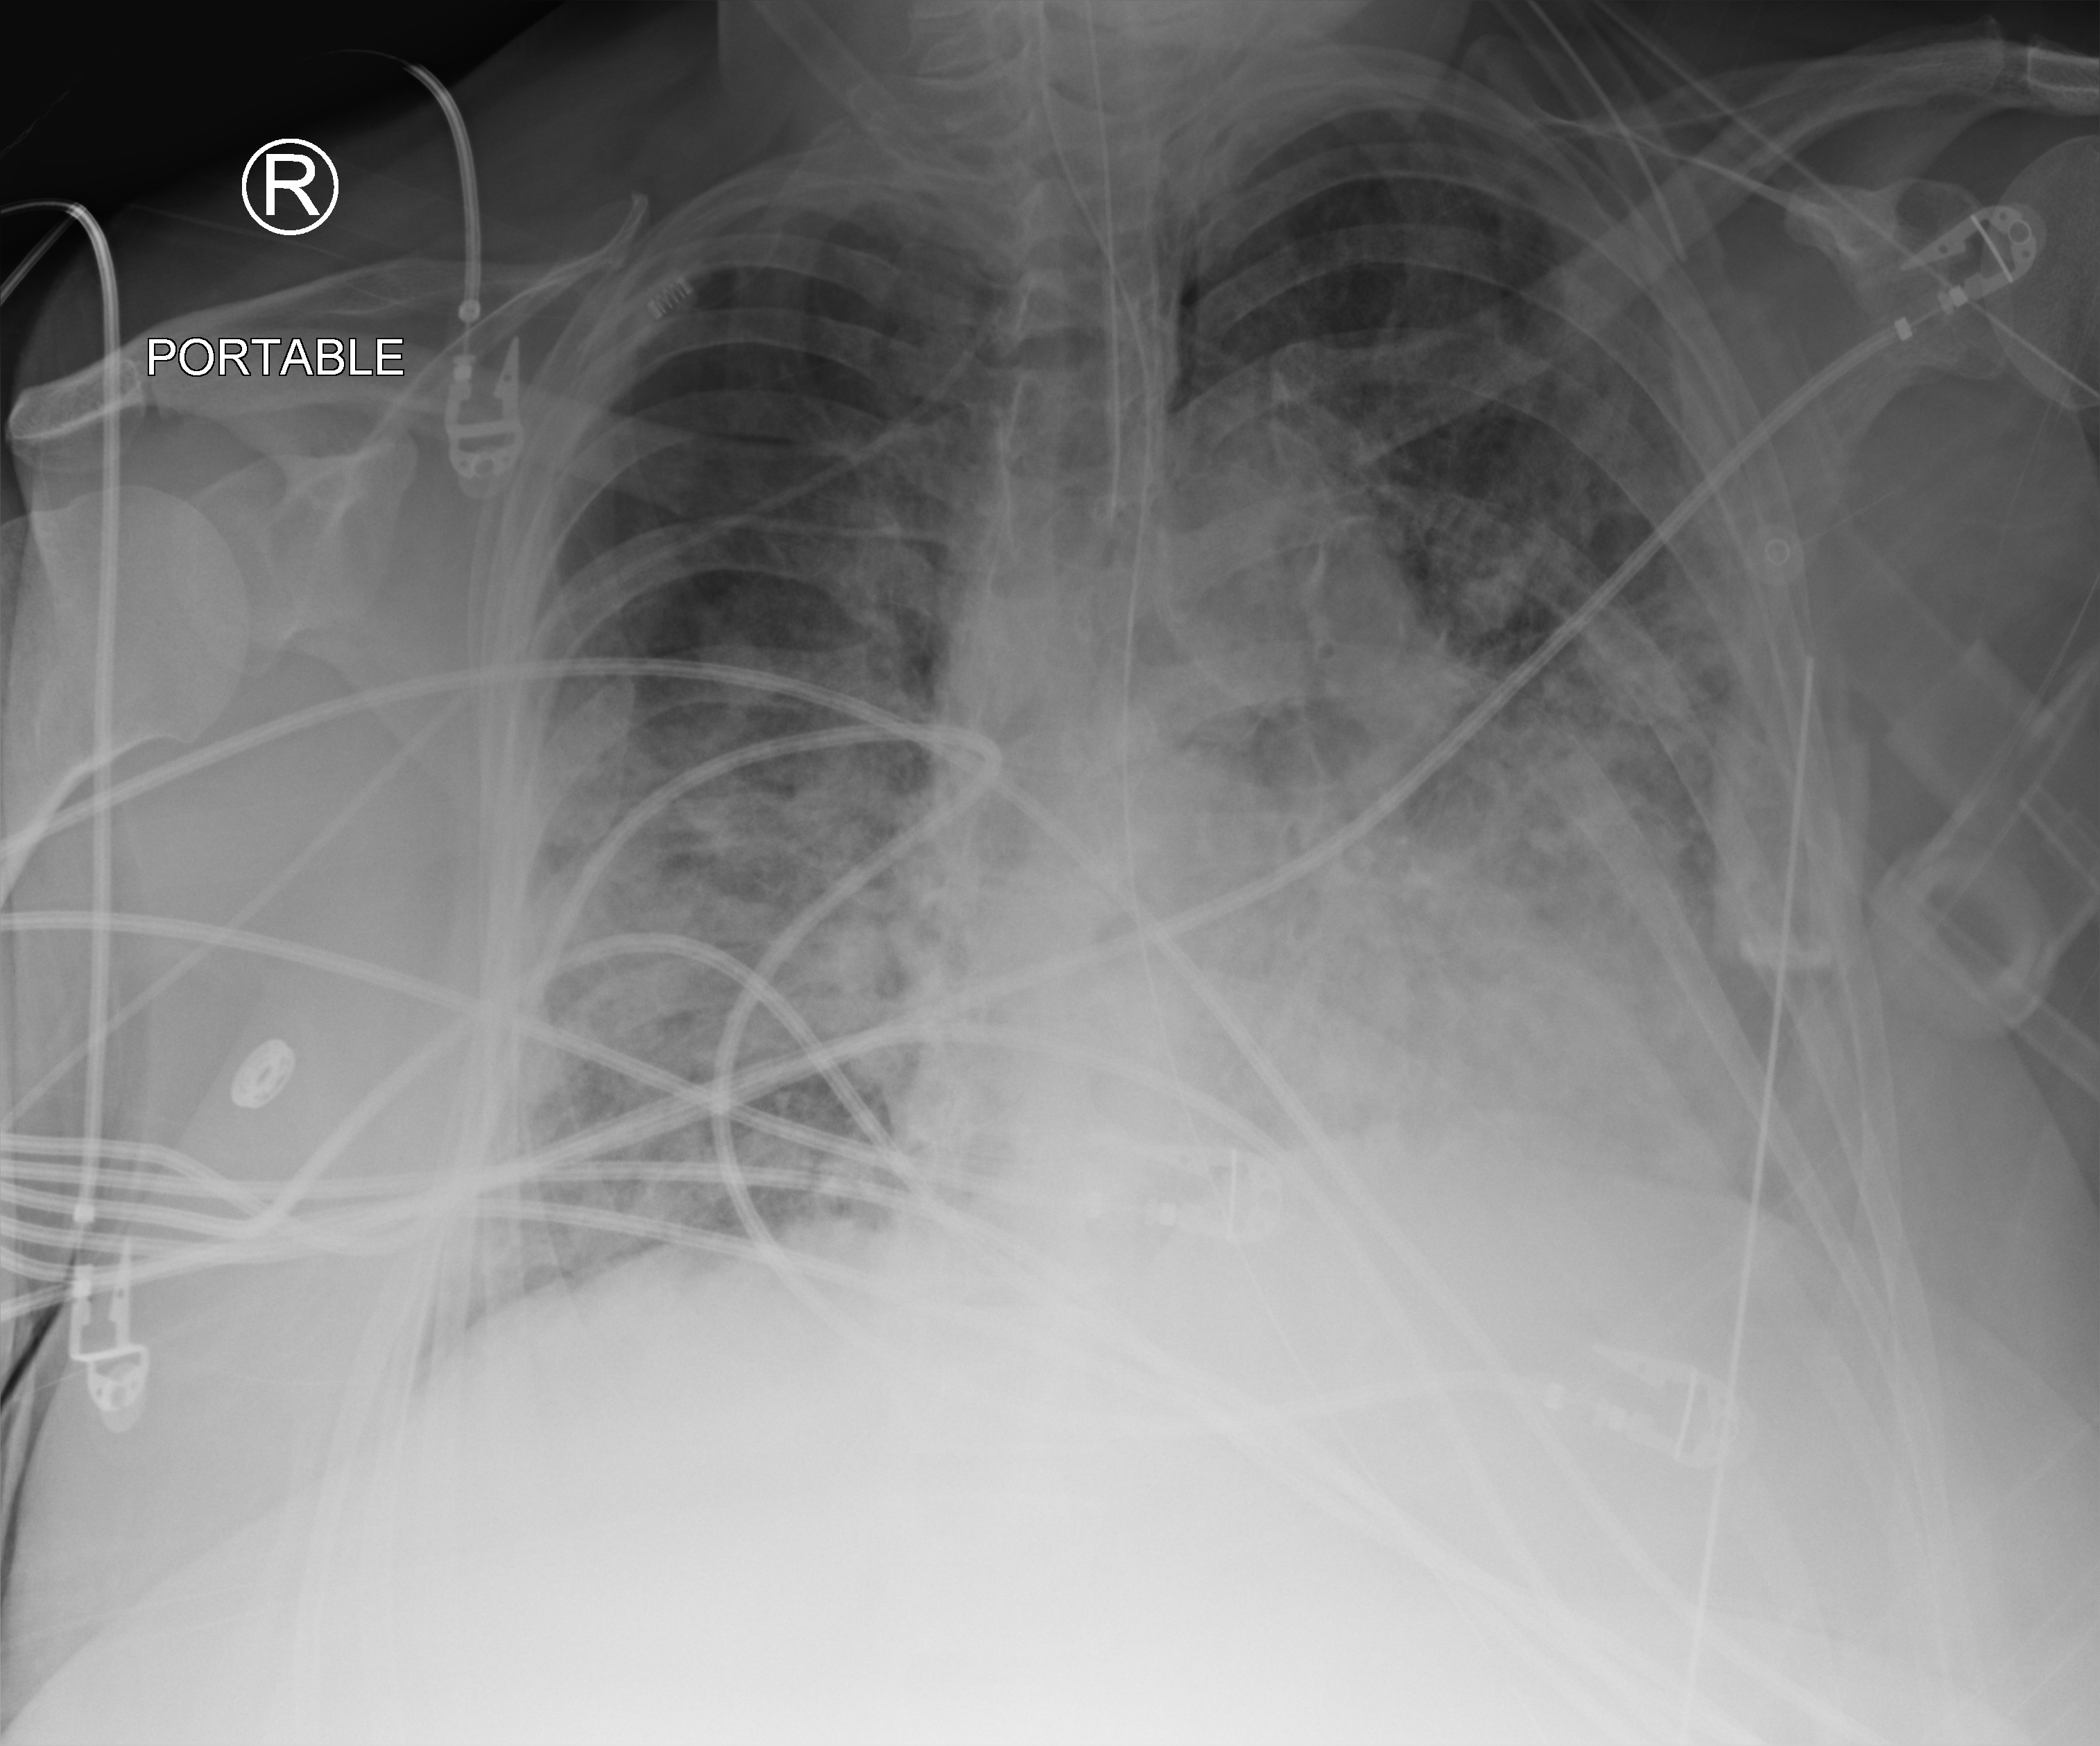
Bedside chest radiograph (computed radiography); anteroposterior (AP) projection. Patient hospitalised with COVID-19; female, aged 60–74 years.
From the hospital-stay record, not from the radiograph (when in the stay this image was taken is not recorded):
- admitted to intensive care during this hospital stay: yes